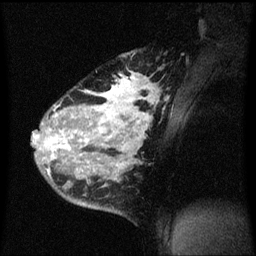
Breast MRI (dynamic contrast-enhanced), one sagittal slice; dynamic contrast-enhanced series, image 2 of 3 at this slice position (ordered by acquisition); 1.5 T; TE 4.2 ms, TR 8.4 ms; 2 mm slice thickness; 256 × 256 image matrix. Patient: female, 34 years. From the clinical record (not read from this slice): setting: breast cancer imaged before/during neoadjuvant chemotherapy; receptor status: HR-positive, HER2-negative.
Structures marked on this image (semi-automatic segmentation, software-assisted and operator-edited):
- analysis volume of interest (the breast-tissue region the enhancement analysis was run in; not a lesion): bounding box <34,50,159,215> (left, top, right, bottom; pixels)
- tumour enhancement mask (voxels above the 70 % enhancement threshold inside the analysis volume of interest): <34,72,157,181>